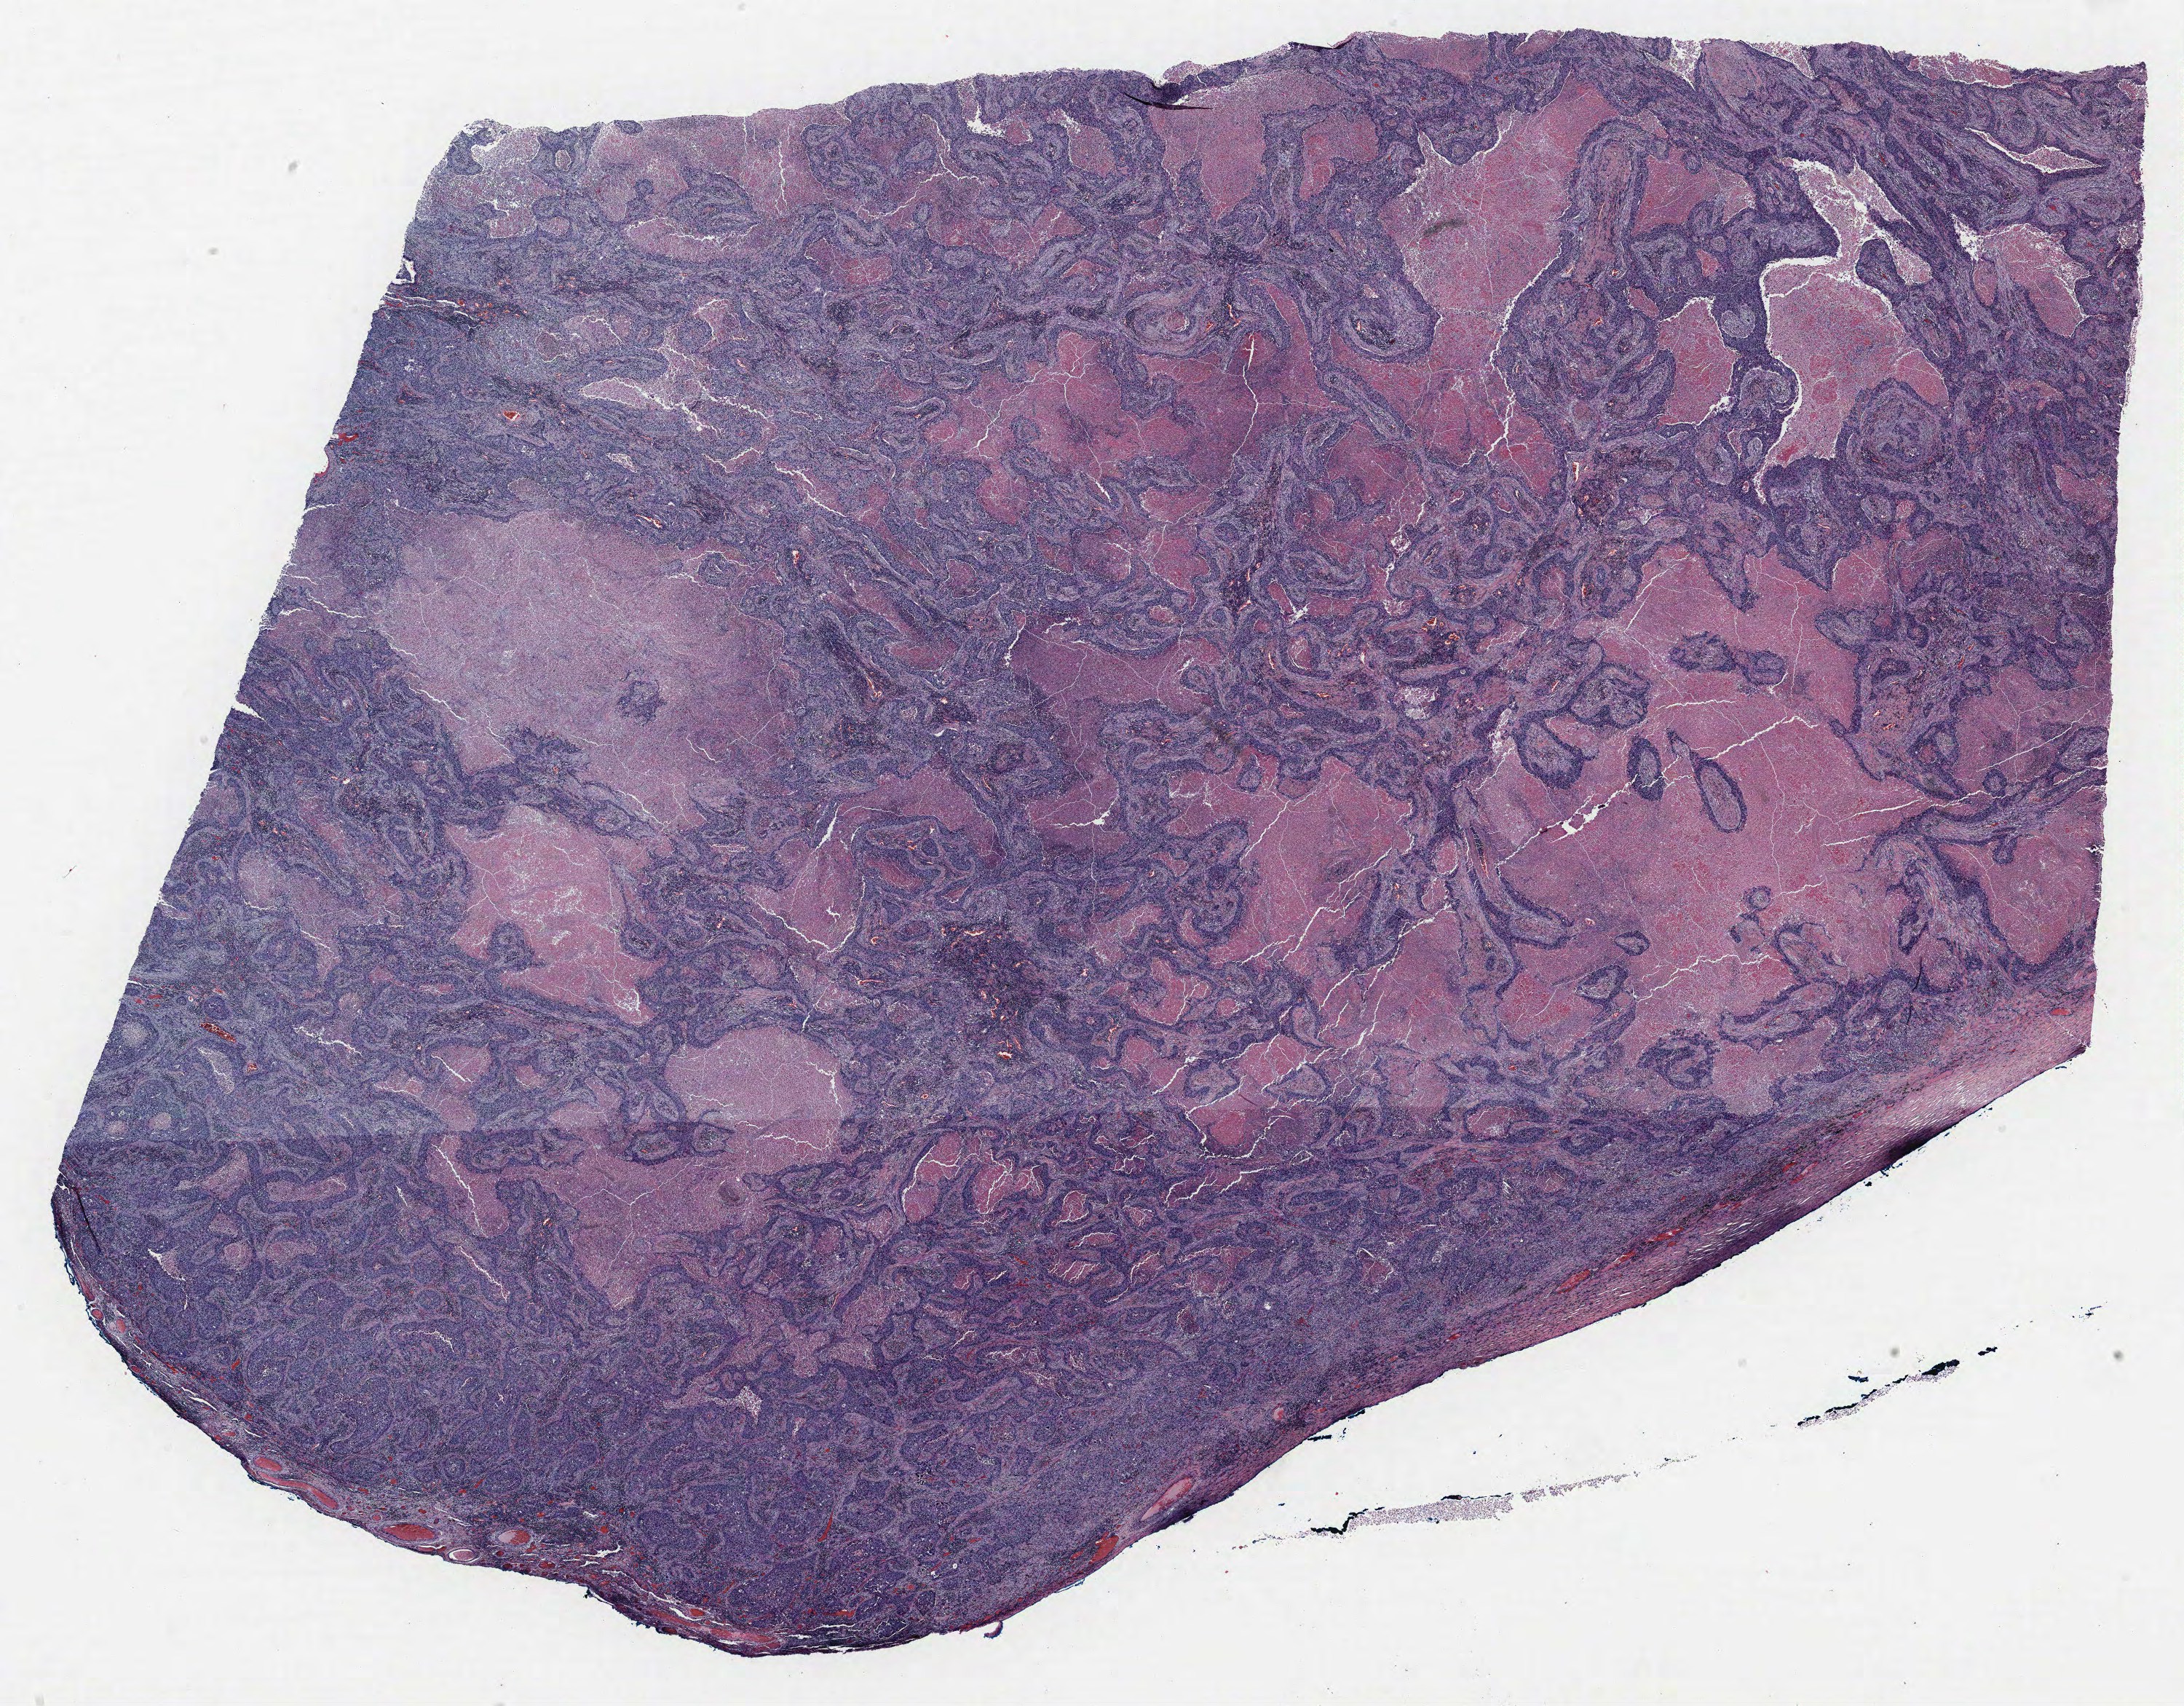
Hematoxylin and eosin (H&E) stained whole-slide image, shown as a low-resolution overview of the whole scanned area (about 24.0 x 18.7 mm). FFPE section. Lung. Female, age 65 at enrolment. Former smoker at enrolment. Grade: moderately differentiated (G2).
- primary tumour location (clinical record): left lower lobe
- stage (AJCC 6th edition): IIB
- ICD-O-3 topography: lower lobe of lung (C34.3)
- tumour size (pathology): 90 mm
- participant's lung-cancer diagnosis: Squamous cell carcinoma, NOS